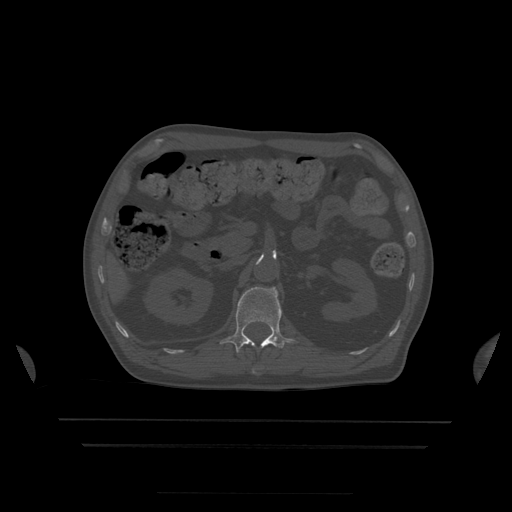
CT including the spine, one axial slice. Bone window (W 1800 / L 400 HU). 1.25 mm slice thickness. 512 × 512 image matrix, field of view 436 × 436 mm. Patient age 68 years. Case-level facts recorded for this patient, not image findings: primary cancer: urothelial.
Annotated regions visible in this slice (semi-automatically segmented with operator editing):
- L1 vertebra: bounding box <221,287,294,353> (left, top, right, bottom; pixels)
- T12 vertebra: <253,371,256,373>